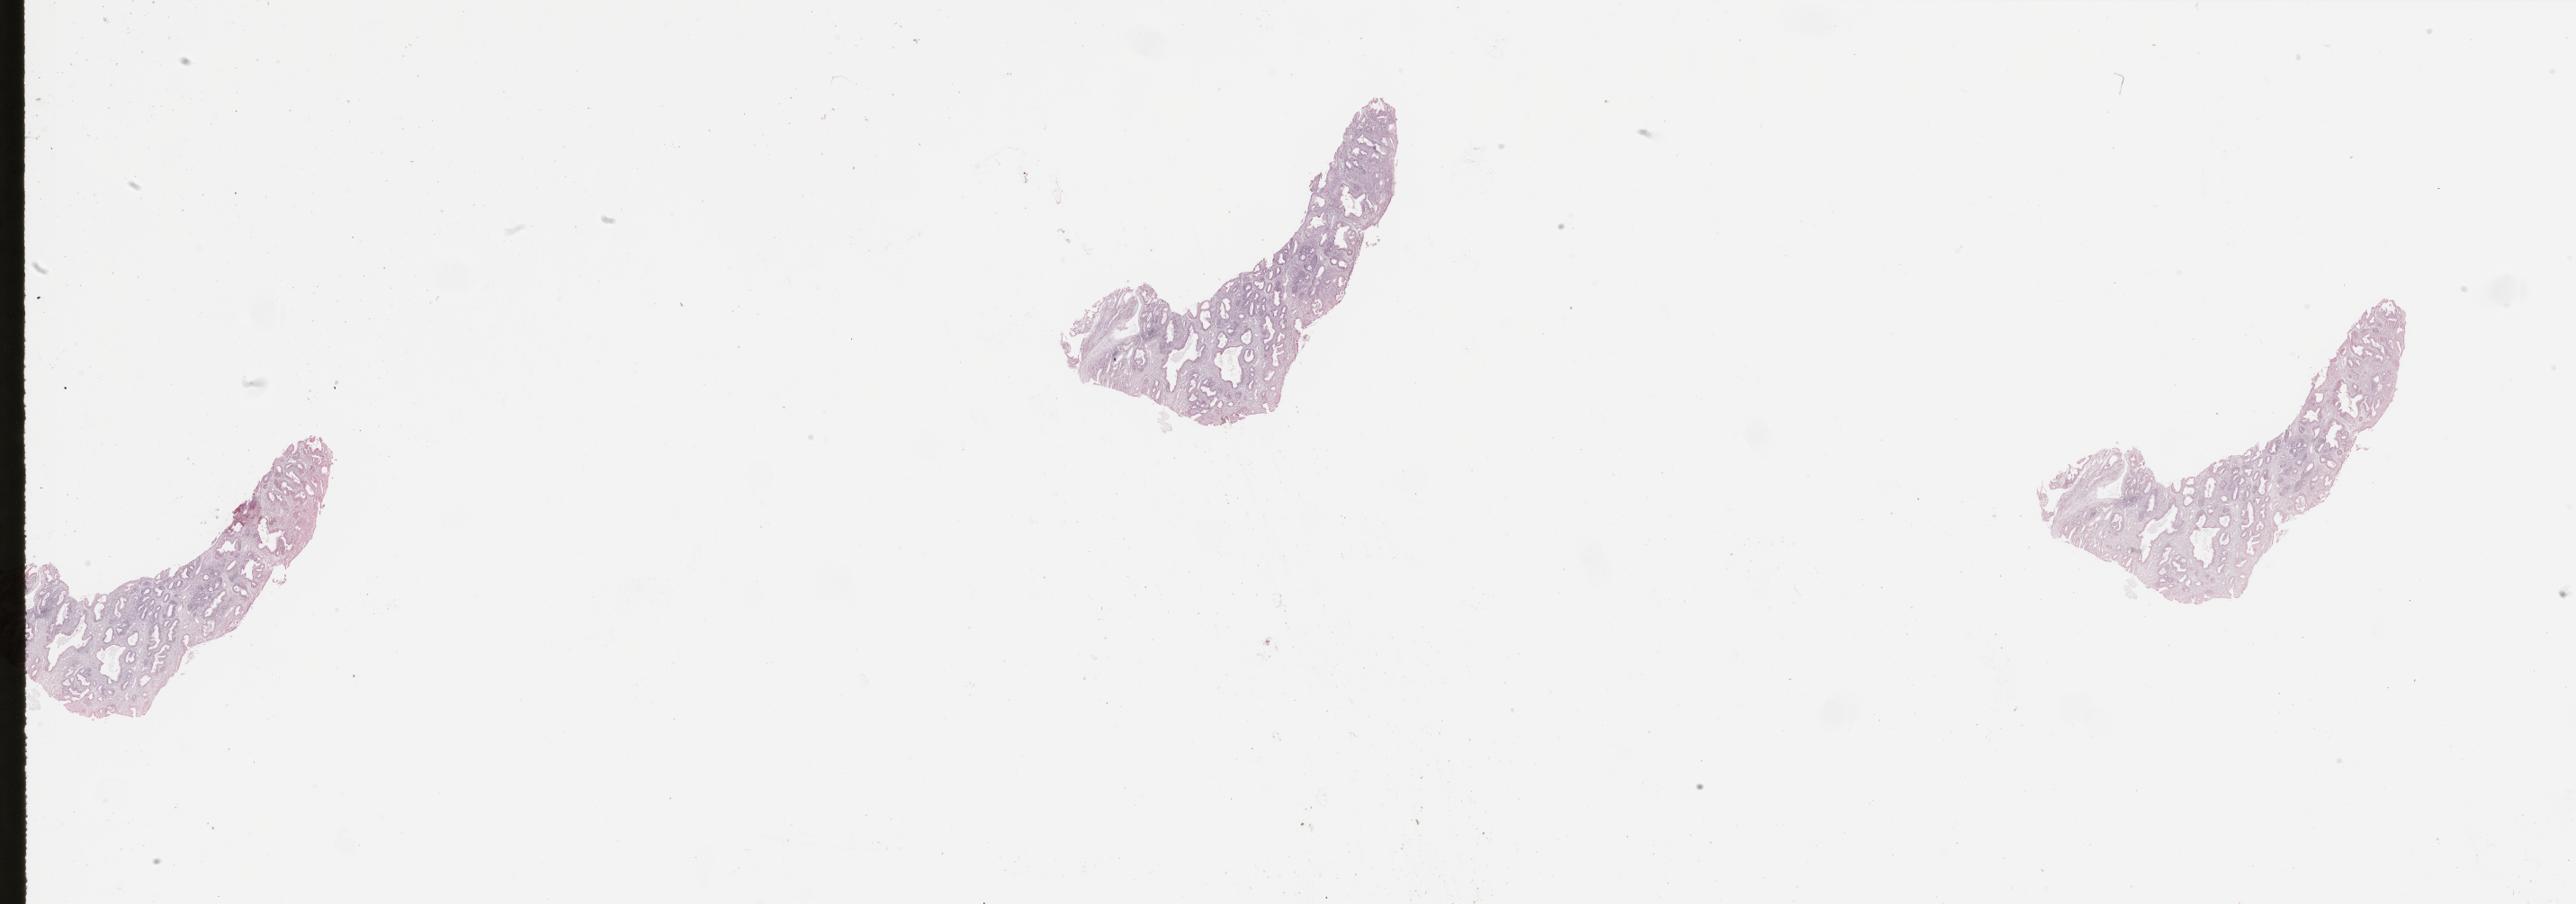
H&E whole-slide image — low-resolution overview of the scanned area, about 45.3 x 15.9 mm (acquisition: 20x scan), tumour tissue sample, sampled site: uterus. 67-year-old female patient. Histologic grade: G1 (well differentiated). Slide review estimates, as recorded: tumour nuclei 80%, necrosis 2%.
* AJCC pathologic stage: I
* primary tumour site (as recorded): anterior endometrium
* diagnosis: Endometrioid adenocarcinoma, NOS